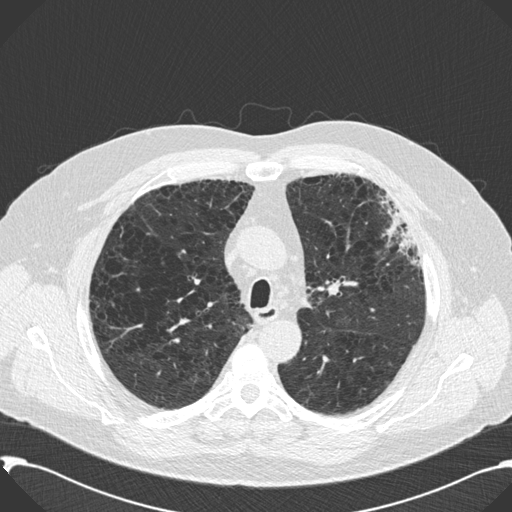
Chest CT (low-dose screening protocol), one axial image. Second annual screen. Lung window (W 1500 / L -600 HU). 120 kVp. Male participant, aged 59 years at enrolment.
Lesion marked by an expert reader, bounding box (x1, y1, x2, y2) in pixels: (361, 196, 425, 292). Screening reader's record for this exam: no non-calcified nodule ≥4 mm recorded. Official screen result: negative screen, significant abnormalities not suspicious for lung cancer. Lung cancer was diagnosed 518 days after this screen: bronchiolo-alveolar carcinoma, mixed mucinous and non-mucinous, left upper lobe, stage IA (AJCC 6th edition), 20 mm at pathology.